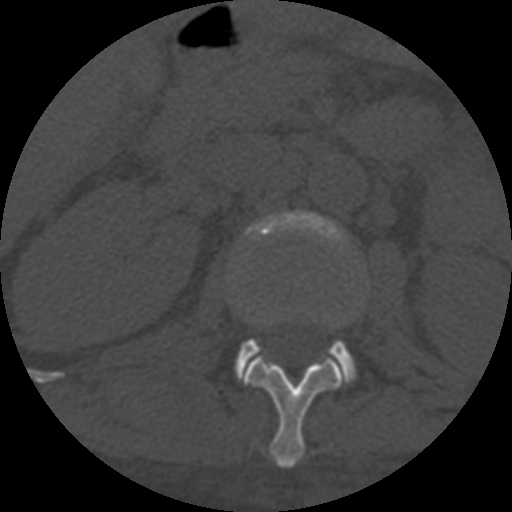
CT including the spine, one axial slice; slice 275 of 708 in the series (ordered by position); 120 kVp; one of 3 acquisitions stored at this slice position; bone window (W 1800 / L 400 HU); 1.25 mm slice thickness; 512 × 512 image matrix. Patient age 55 years. From the clinical record (not read from this slice): primary cancer: colon.
Outlined on this slice (semi-automatic segmentation, software-assisted and operator-edited):
- L1 vertebra: bounding box <241,319,346,467> (left, top, right, bottom; pixels)
- L2 vertebra: <235,211,355,379>